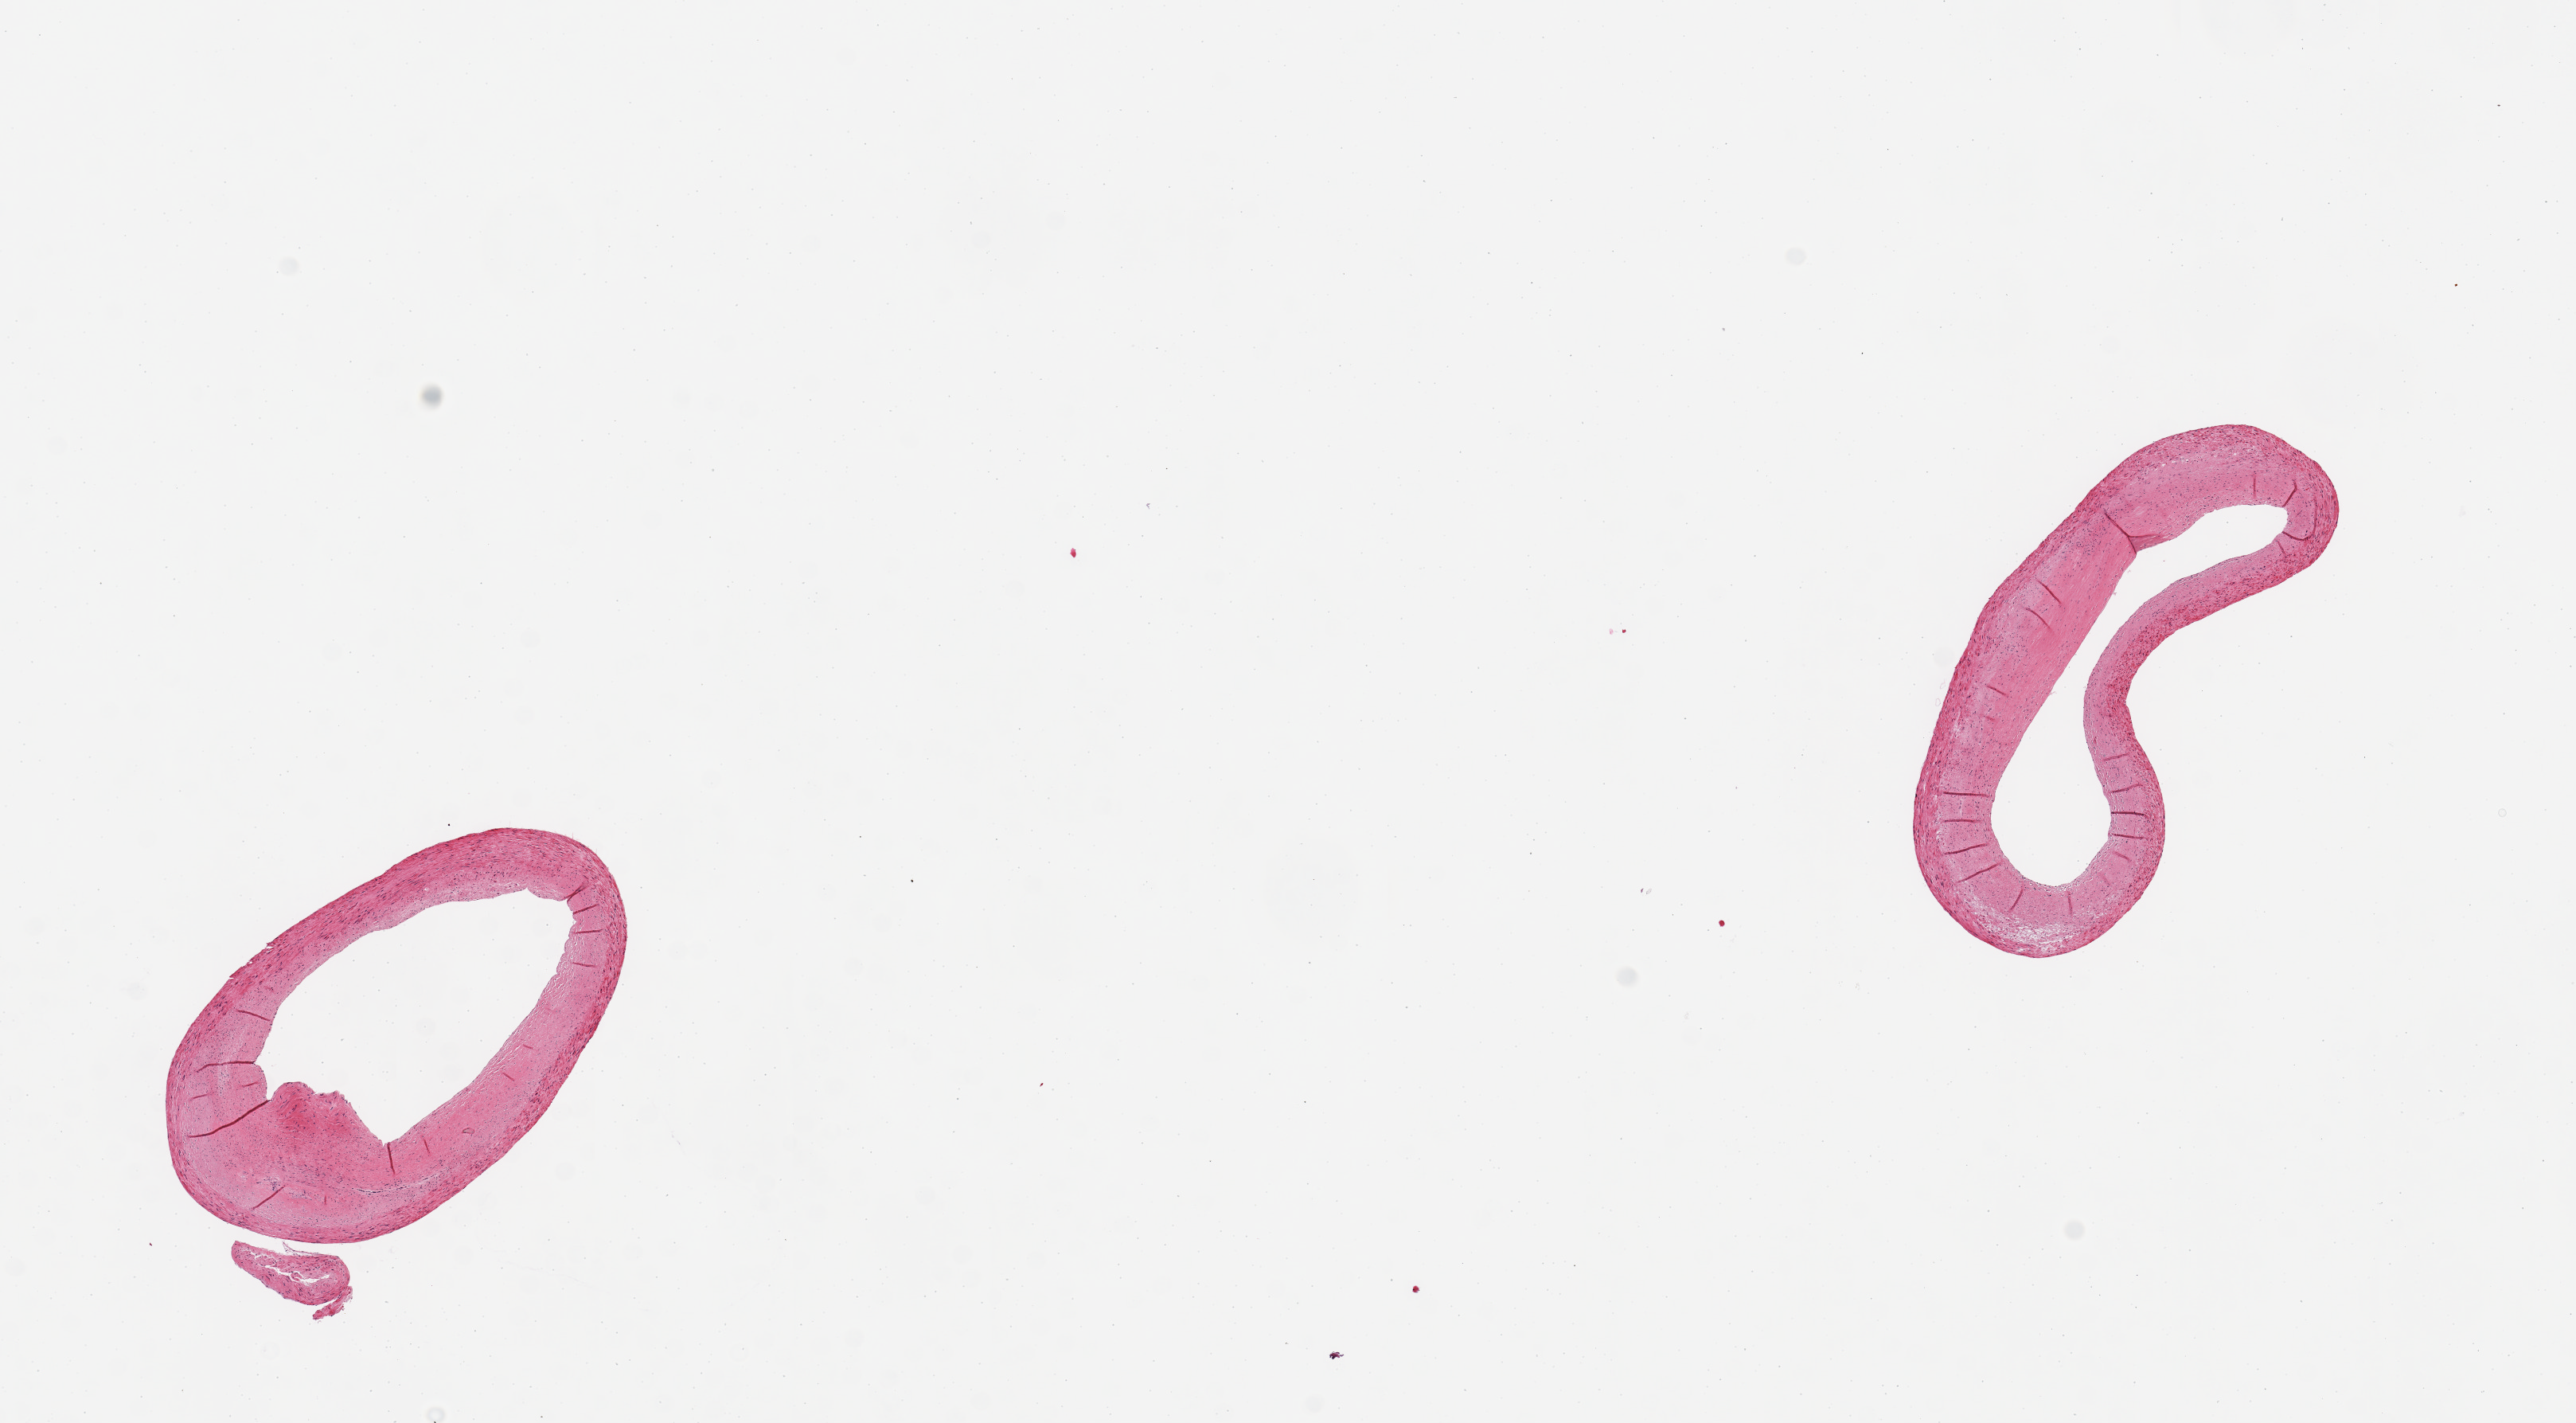
Digitized hematoxylin and eosin (H&E)-stained section — whole scanned area (about 12.8 x 7.1 mm, acquisition: 20x scan) shown as a low-resolution overview; PAXgene-fixed, paraffin-embedded tissue; section of coronary artery (target tissue); tissue donor sample. Donor: male.
Pathologist's review note for this sample: 2 pieces; widely patent arteries with flat fibrous intimal plaques; well trimmed of adventitial tissue.